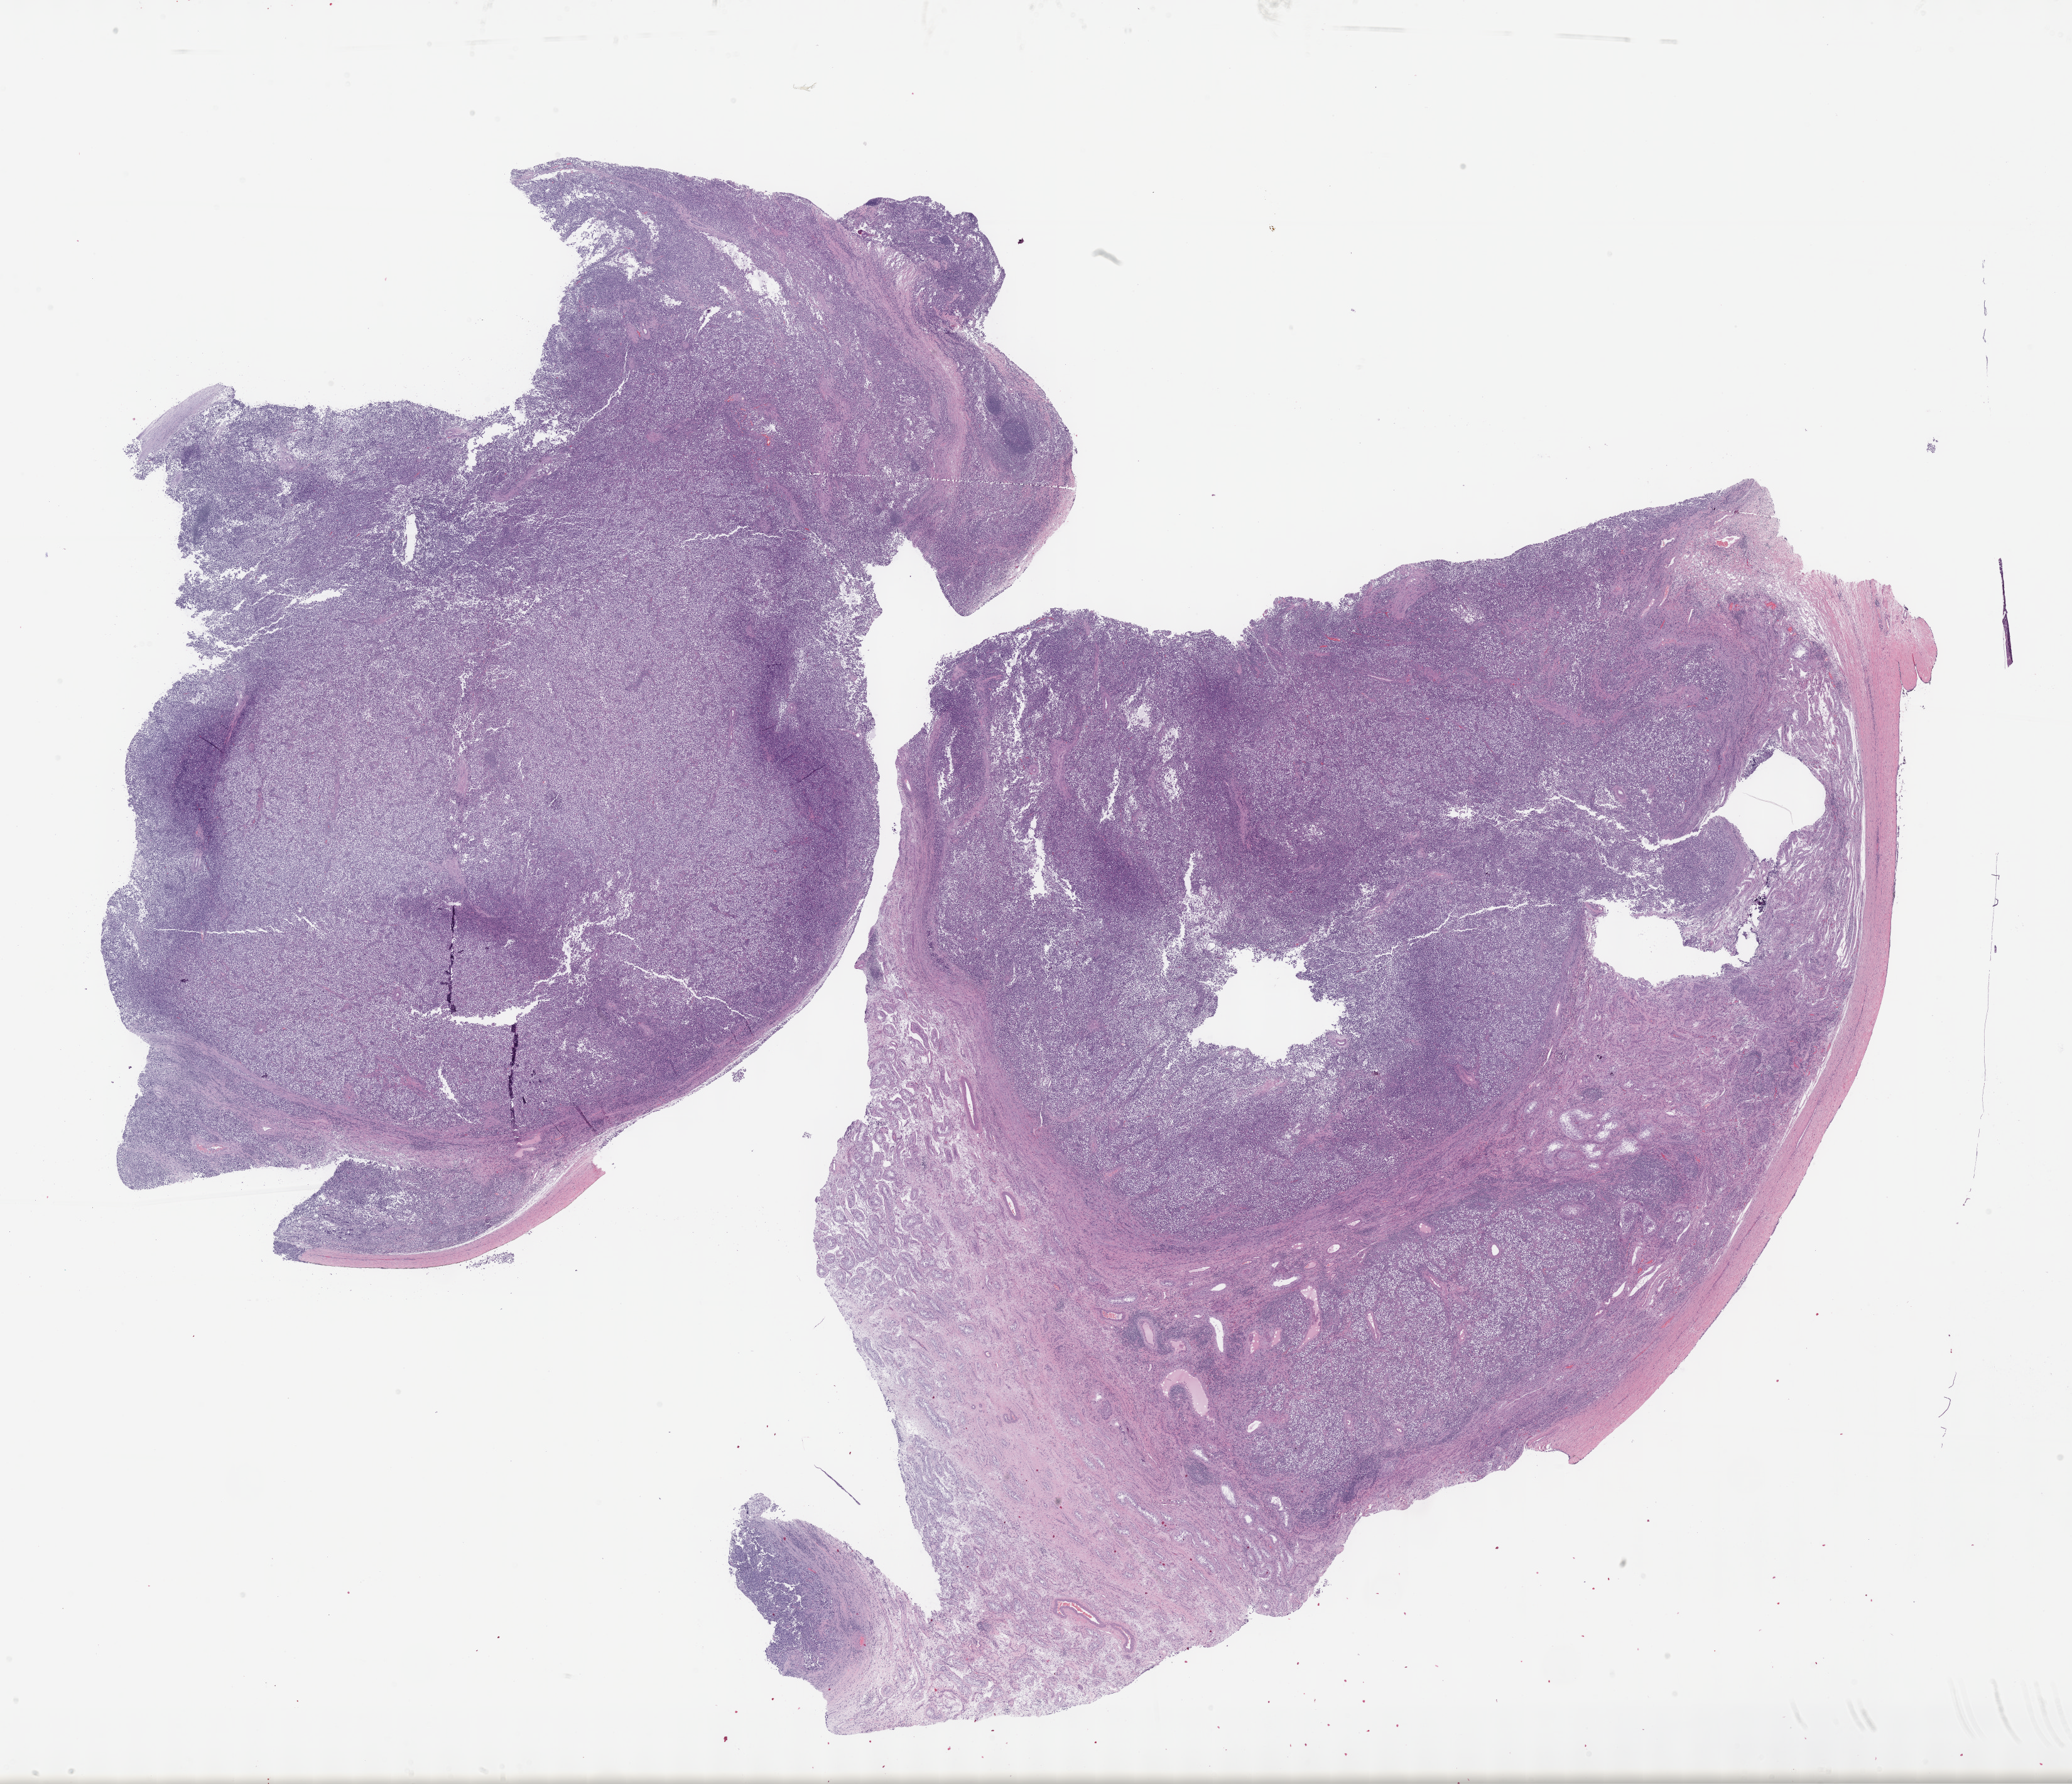
H&E whole-slide image, low-resolution overview of the scanned area, about 26.7 x 23.0 mm, formalin-fixed paraffin-embedded (FFPE) diagnostic section, primary tumour sample from the testis. Patient: male, age at initial diagnosis 22 years.
• pathologic diagnosis: Seminoma, NOS
• TNM: T1 NX M0
• AJCC pathologic stage: IA